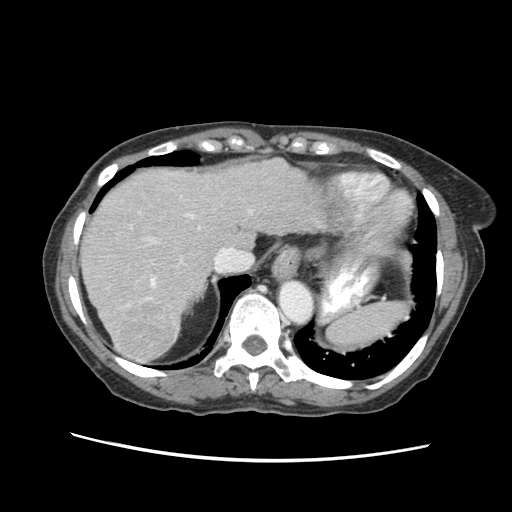
Contrast-enhanced abdominal CT (liver protocol), one axial slice; position 47 of 63 along the scan axis; reconstruction kernel STANDARD; soft-tissue window (W 400 / L 40 HU); 512 × 512 image matrix, field of view 340 × 340 mm. Case-level facts recorded for this patient, not image findings: diagnosis: hepatocellular carcinoma (patient treated with transarterial chemoembolisation; whether this scan precedes or follows treatment is not stated here); TNM stage (as recorded): Stage-I; Child-Pugh class: B; tumour differentiation: well differentiated; tumour nodularity: uninodular.
Structures marked on this image (semi-automatic segmentation, software-assisted and operator-edited):
- liver parenchyma outside the tumour (the mass and vessels are separate outlines, so this box may not span the whole liver): bounding box [x1, y1, x2, y2] px = [80, 156, 390, 360]
- mass: [114, 302, 176, 359]
- liver vessels: [140, 211, 198, 300]